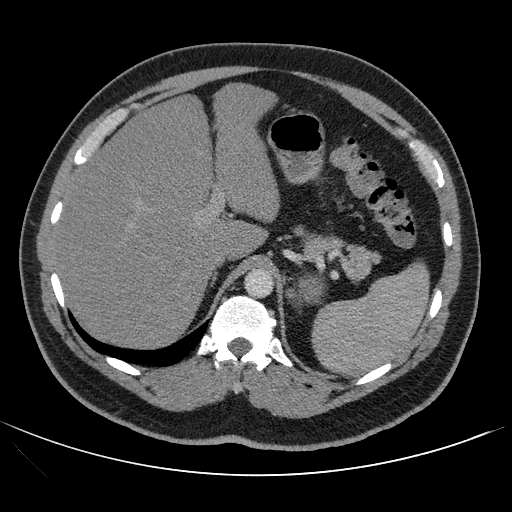
Contrast-enhanced abdominal CT, one axial slice; intravenous contrast given; soft-tissue window (W 400 / L 40 HU); 2.5 mm slice thickness; 512 × 512 image matrix, field of view 399 × 399 mm. Male patient, age 53 years. From the clinical record (not read from this slice): diagnosis: adrenocortical carcinoma; tumour side: left adrenal; tumour size at pathology: 7.9 cm; Ki-67 index: 20 %; stage (as recorded): 2.
Outlined on this slice (semi-automatically segmented with operator editing):
- mass: box from (x=299, y=280) to (x=325, y=304) px